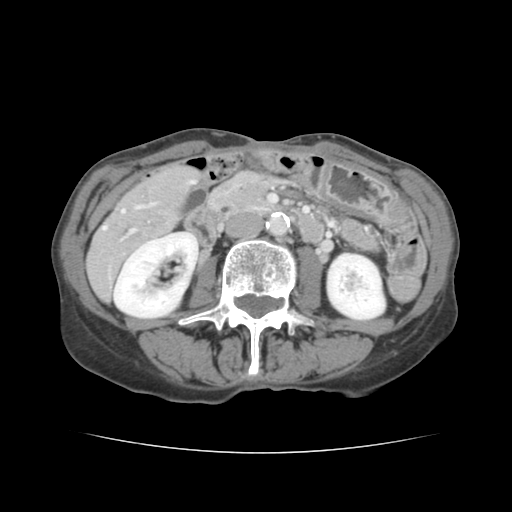
Contrast-enhanced abdominal CT, one axial slice. Slice 44 of 136 in the series (ordered by position). Intravenous contrast given. Soft-tissue window (W 400 / L 40 HU). 2.5 mm slice thickness. 512 × 512 image matrix. Female patient, age 77 years. From the clinical record (not read from this slice): diagnosis: colorectal cancer liver metastases, imaged before liver resection; multiple liver metastases: yes; largest metastasis: 3 cm; disease in both lobes: no.
Structures marked on this image (outlined manually by an expert reader):
- hepatic veins: bounding box [x1, y1, x2, y2] px = [103, 181, 194, 230]
- liver: [89, 166, 199, 297]
- planned liver remnant (the part of the liver to remain after resection): [175, 167, 197, 185]
- portal vein (with intrahepatic branches): [131, 229, 135, 232]